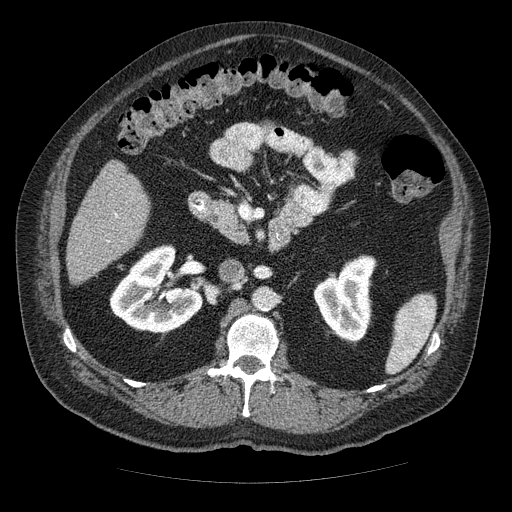
Contrast-enhanced abdominal CT (liver protocol), one axial slice; slice 17 of 85 in the series (ordered by position); soft-tissue window (W 400 / L 40 HU); 2.5 mm slice thickness; 512 × 512 image matrix, field of view 420 × 420 mm. From the clinical record (not read from this slice): diagnosis: hepatocellular carcinoma (patient treated with transarterial chemoembolisation; whether this scan precedes or follows treatment is not stated here); TNM stage (as recorded): Stage-IIIA; Child-Pugh class: A; tumour nodularity: multinodular; tumour size: 7 cm.
Outlined on this slice (semi-automatically segmented with operator editing):
- liver parenchyma outside the tumour (the mass and vessels are separate outlines, so this box may not span the whole liver): bounding box <66,160,148,284> (left, top, right, bottom; pixels)
- liver vessels: <108,214,118,242>